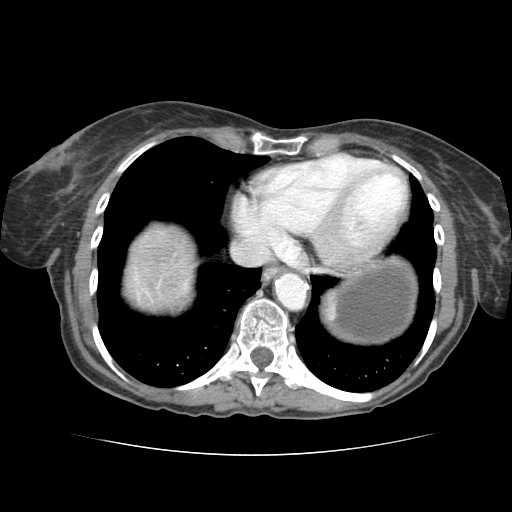
Contrast-enhanced abdominal CT (liver protocol), one axial slice. Slice 74 of 77 in the series (ordered by position). Reconstruction kernel STANDARD. Soft-tissue window (W 400 / L 40 HU). 512 × 512 image matrix, field of view 340 × 340 mm. Case-level facts recorded for this patient, not image findings: diagnosis: hepatocellular carcinoma (patient treated with transarterial chemoembolisation; whether this scan precedes or follows treatment is not stated here); TNM stage (as recorded): Stage-I; Child-Pugh class: A; tumour differentiation: well differentiated; tumour nodularity: uninodular.
Annotated regions visible in this slice (semi-automatic segmentation, software-assisted and operator-edited):
- liver parenchyma outside the tumour (the mass and vessels are separate outlines, so this box may not span the whole liver): box from (x=134, y=234) to (x=184, y=298) px